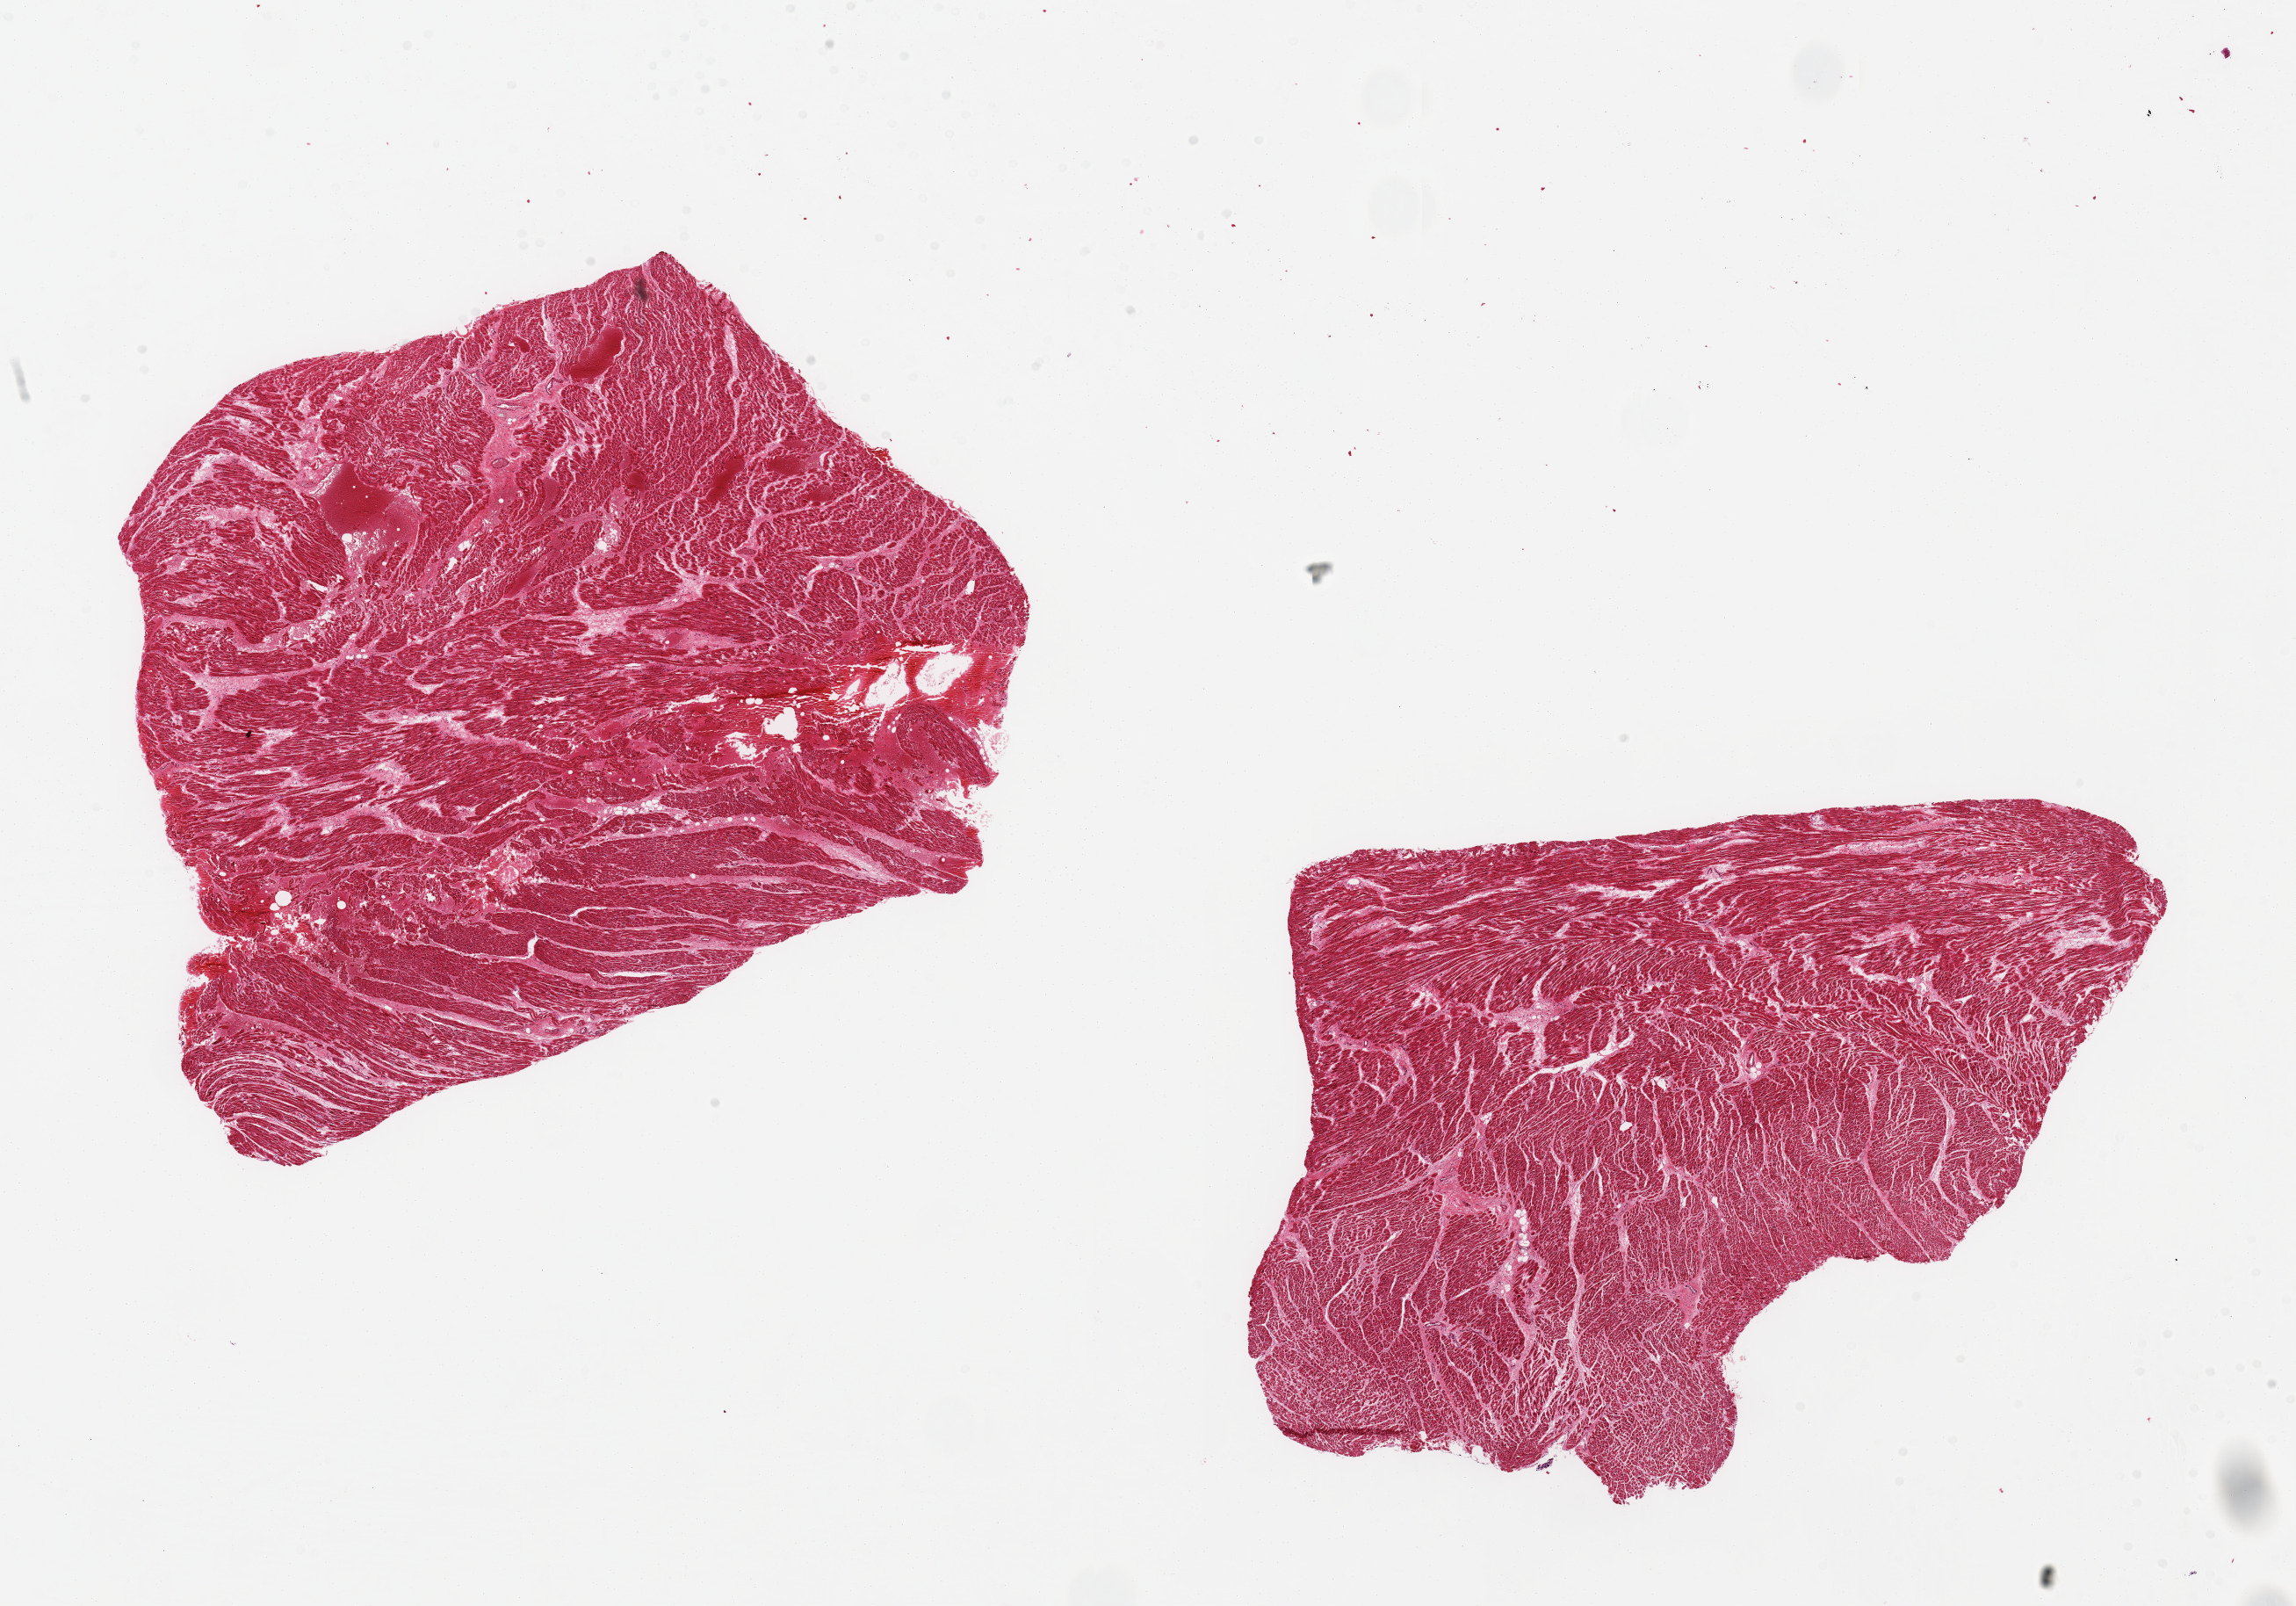
Digitized H&E-stained section, low-resolution overview of the scanned area, about 20.7 x 14.5 mm (slide scanned at 20x), PAXgene-fixed, paraffin-embedded tissue, sampled site (target tissue): heart, donor tissue sample. Male donor.
Review note (as recorded): 2 pieces, ~8x6mm. Mild interstital fibrosis.chronic ischemic changes.